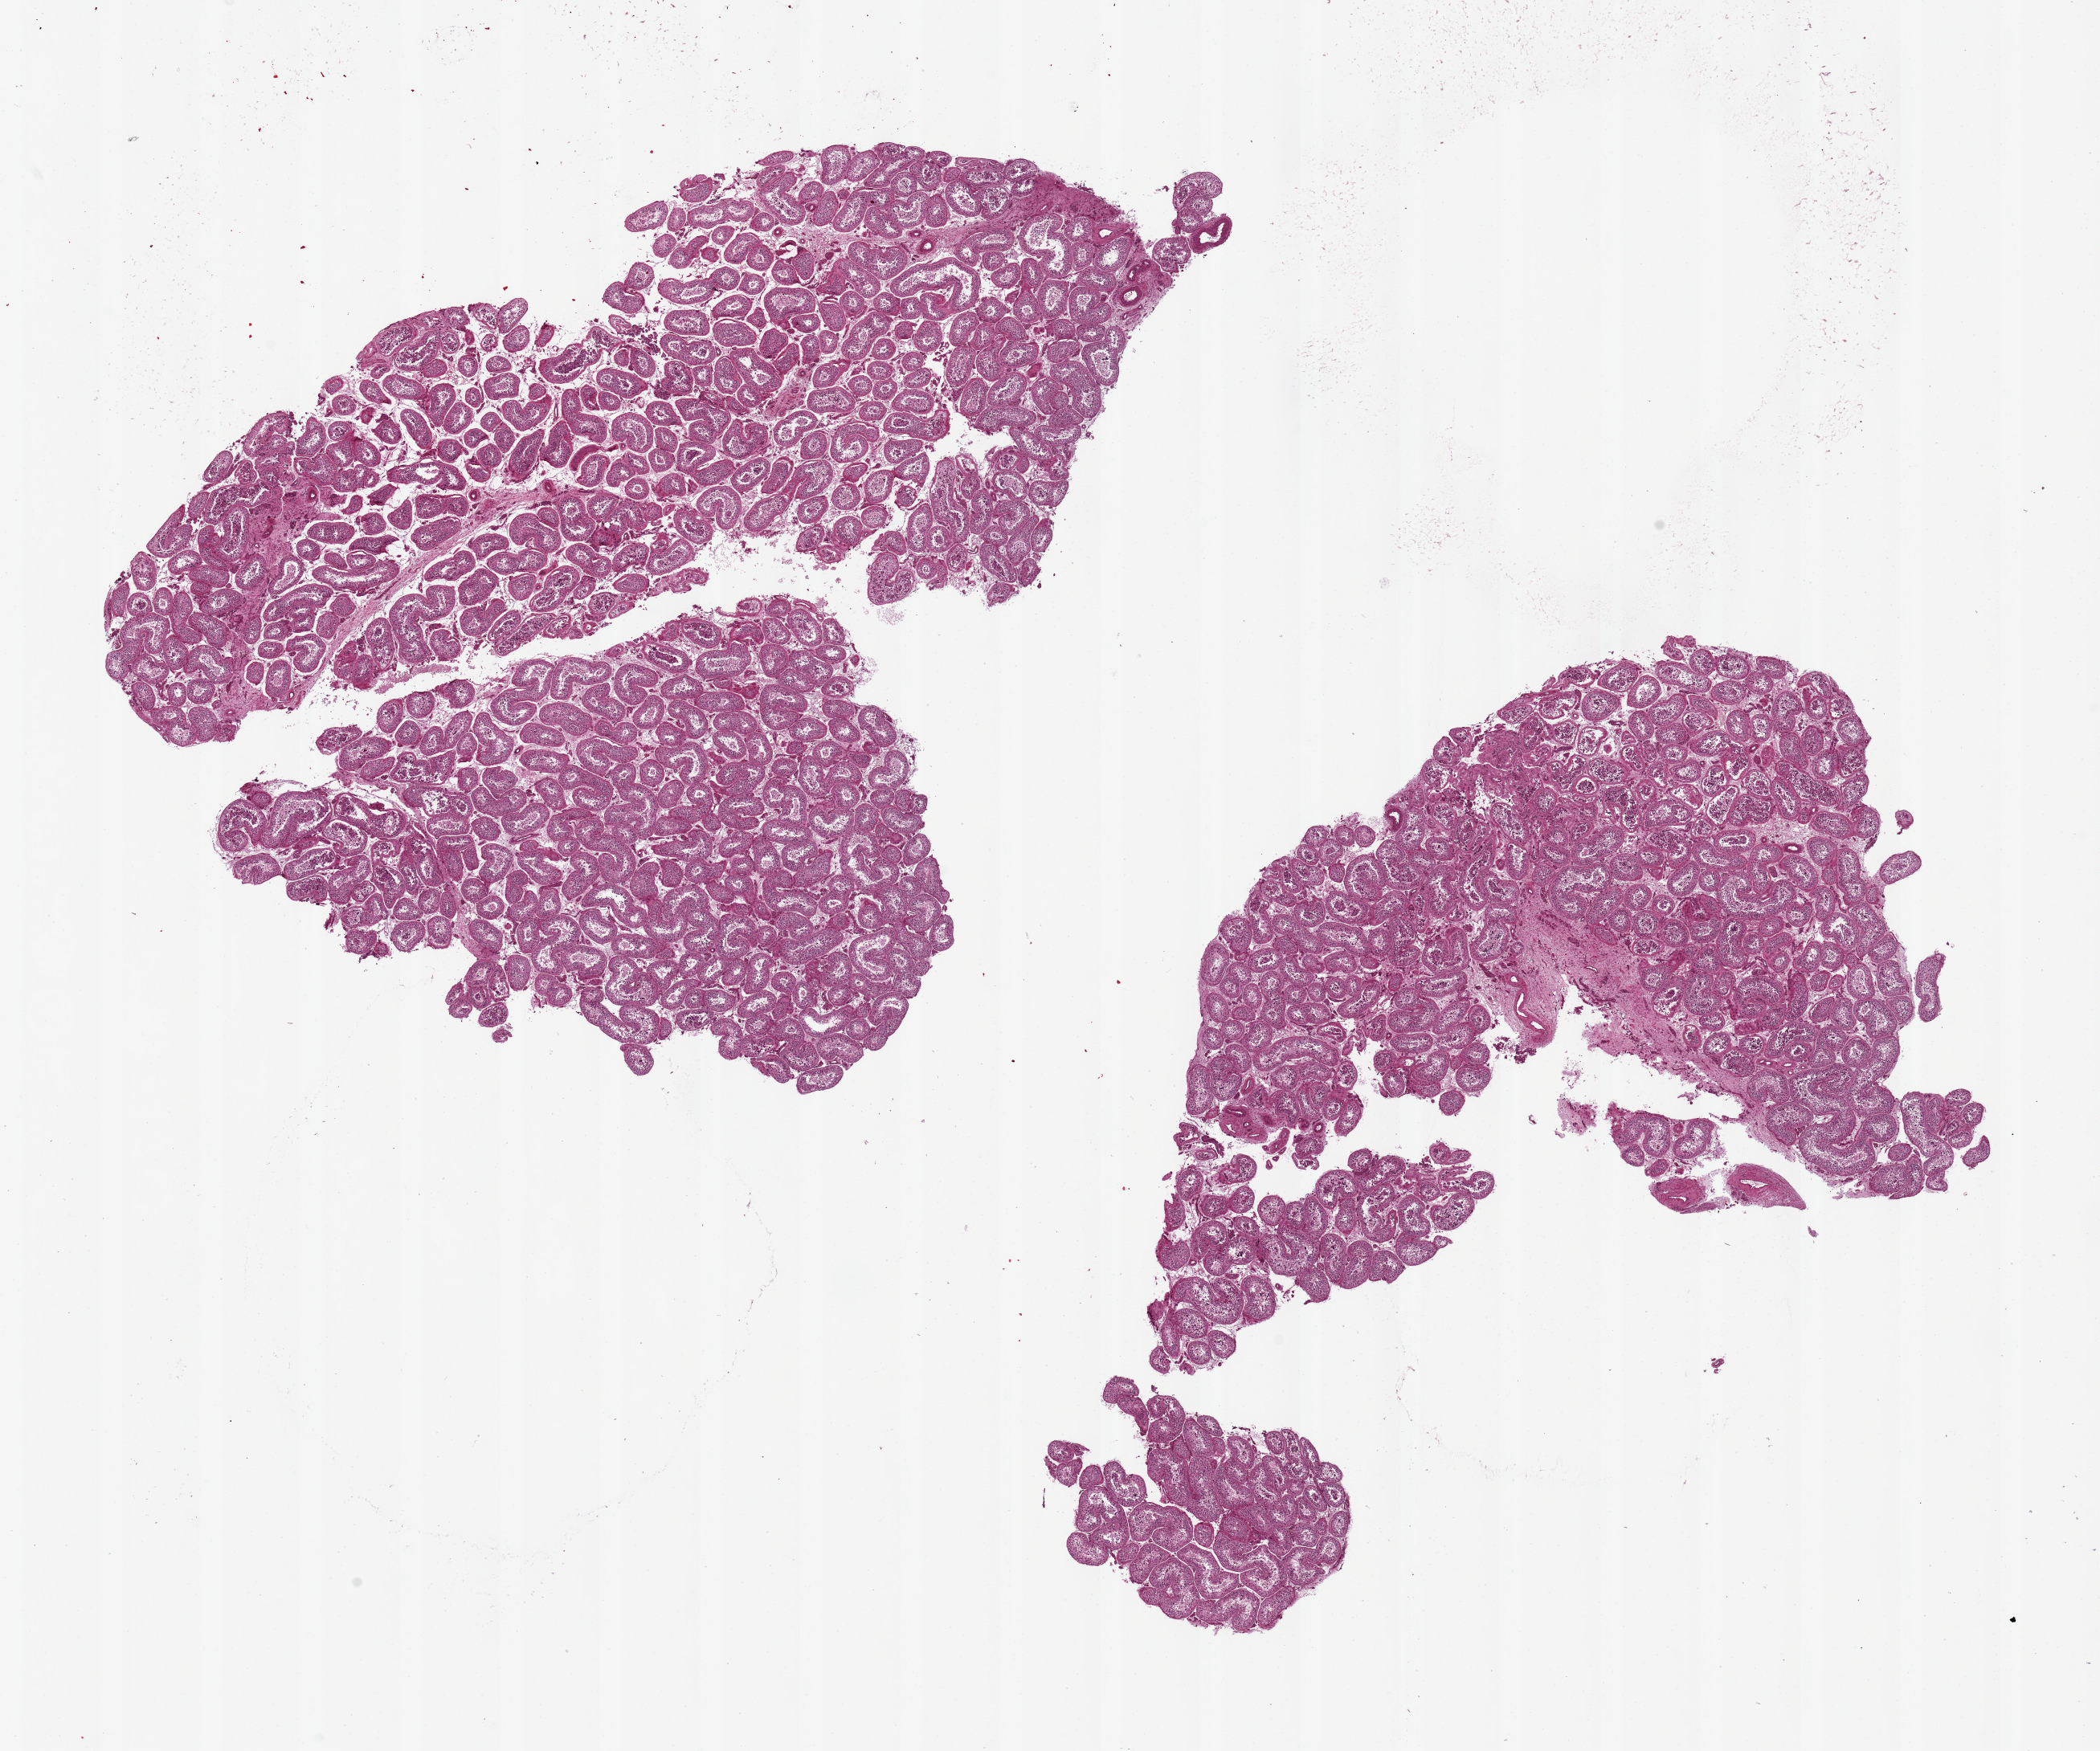
Digitized H&E-stained section, brightfield — low-resolution overview of the scanned area, about 20.7 x 17.2 mm (acquisition: 20x scan), PAXgene-fixed, paraffin-embedded tissue, sampled site (target tissue): testis, tissue donor sample. Male donor.
Review note (as recorded): 2 pieces, 12x9 7 11x7mm; spermatogenesis.